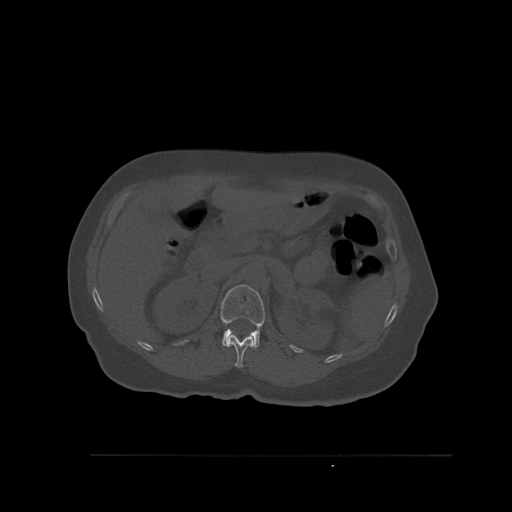
CT including the spine, one axial slice; position 274 of 527 along the scan axis; bone window (W 1800 / L 400 HU); 1.5 mm slice thickness; 512 × 512 image matrix, field of view 470 × 470 mm. Female patient, age 73 years. From the clinical record (not read from this slice): primary cancer: breast; vertebrae with lytic lesions (as recorded): L2.
Structures marked on this image (semi-automatically segmented with operator editing):
- L1 vertebra: bounding box [x1, y1, x2, y2] px = [220, 284, 265, 348]
- T12 vertebra: [227, 333, 254, 368]